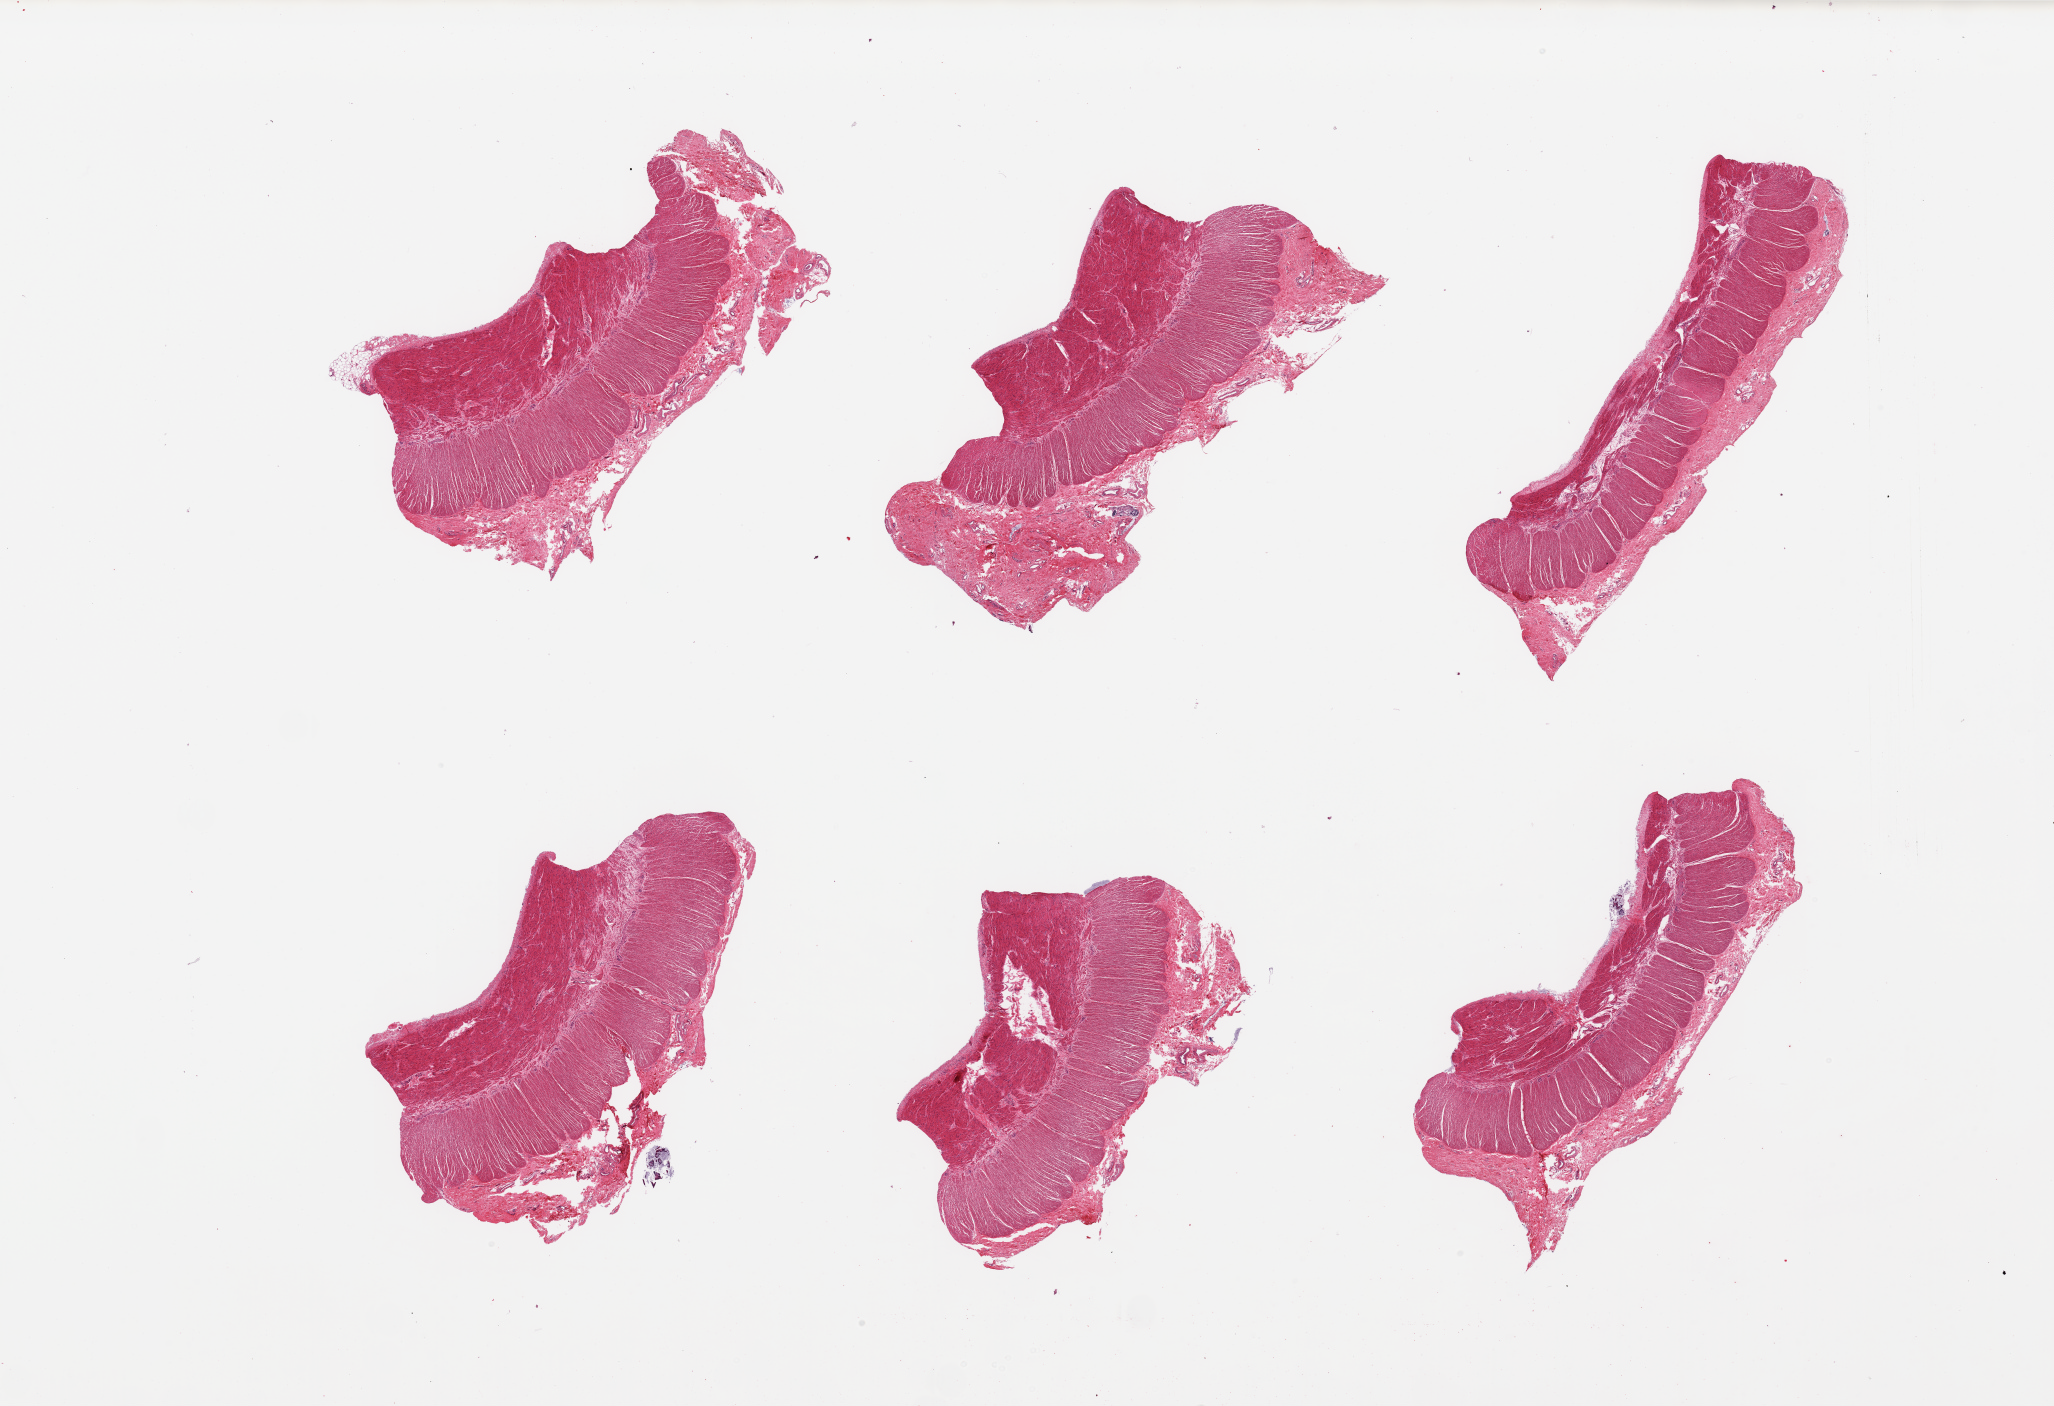
Digitized H&E-stained section — low-resolution overview of the scanned area, about 32.5 x 22.2 mm (slide scanned at 20x). PAXgene-fixed, paraffin-embedded tissue. Sampled site (target tissue): sigmoid colon. Tissue donor sample. Donor: female.
* pathologist's review note for this sample: 6 pieces; target muscularis